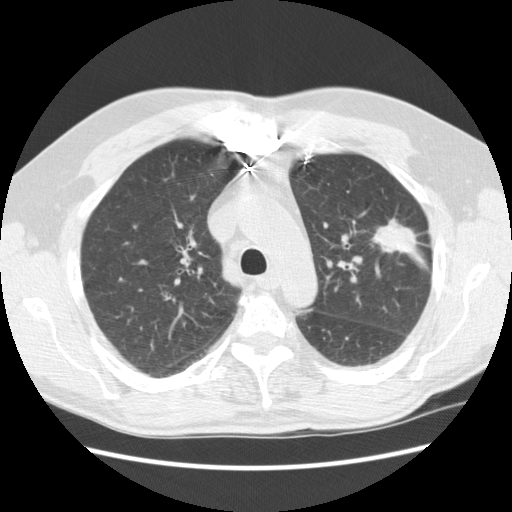
Axial slice from a low-dose chest CT screening exam. Baseline screening round. Lung window (W 1500 / L -600 HU). Standard (soft-tissue) reconstruction kernel (STANDARD). Slice 172 of 231 in the series. Male participant, aged 72 years at enrolment. Former smoker at enrolment.
- Expert-annotated lung lesion, box from (x=354, y=204) to (x=429, y=259) px.
- The exam's reader record, not a measurement of the box and not confirmed to be the same lesion: non-calcified nodule or mass ≥4 mm, left upper lobe, 25 × 18 mm, spiculated (stellate) margins, soft tissue attenuation.
- Official screen result: positive, change unspecified: nodule(s) >= 4 mm or enlarging nodule(s), mass(es), or other non-specific abnormalities suspicious for lung cancer.
- Later outcome: lung cancer diagnosed 35 days after this screen — adenocarcinoma, NOS, left upper lobe, well differentiated (G1), stage IIIB (AJCC 6th edition), 25 mm at pathology.